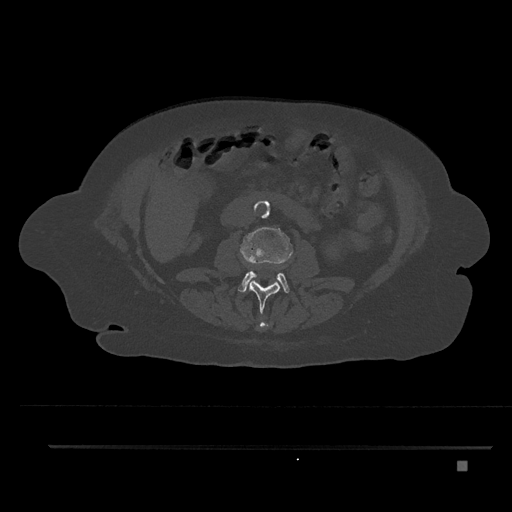
CT including the spine, one axial slice; position 156 of 797 along the scan axis; 120 kVp; bone window (W 1800 / L 400 HU); 0.5 mm slice thickness; 512 × 512 image matrix. Female patient, age 76 years. From the clinical record (not read from this slice): primary cancer: lung; vertebrae with lytic lesions (as recorded): T11, L3.
Structures marked on this image (semi-automatically segmented with operator editing):
- L1 vertebra: box from (x=258, y=322) to (x=269, y=330) px
- L2 vertebra: (x=248, y=280)–(x=280, y=328)
- L3 vertebra: (x=238, y=227)–(x=293, y=293)